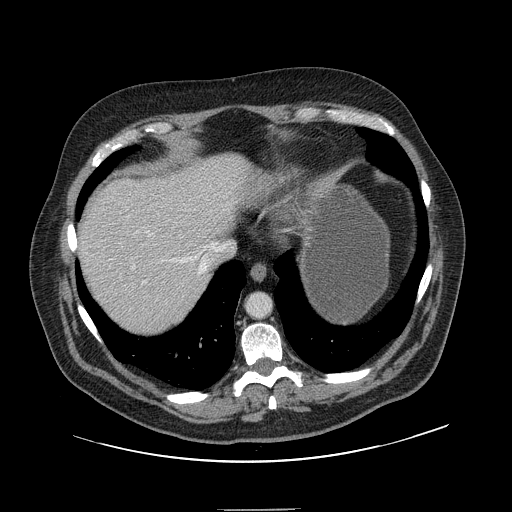
Contrast-enhanced abdominal CT, one axial slice. Position 127 of 154 along the scan axis. Intravenous contrast given. Soft-tissue window (W 400 / L 40 HU). 512 × 512 image matrix, field of view 451 × 451 mm. Male patient, age 61 years. From the clinical record (not read from this slice): diagnosis: colorectal cancer liver metastases, imaged before liver resection; multiple liver metastases: yes; largest metastasis: 2.6 cm.
Annotated regions visible in this slice (outlined manually by an expert reader):
- hepatic veins: bounding box <175,242,215,274> (left, top, right, bottom; pixels)
- liver: <77,154,244,335>
- planned liver remnant (the part of the liver to remain after resection): <77,154,245,335>
- portal vein (with intrahepatic branches): <127,215,145,284>